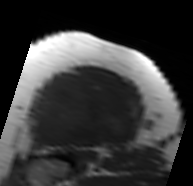
MRI of an extremity soft-tissue mass, one axial slice. Position 56 of 91 along the scan axis. MR volume resampled by the dataset authors to the PET/CT grid (not the native acquisition matrix). 3.27 mm slice thickness. 193 × 186 image matrix. Female patient. From the clinical record (not read from this slice): histological type: malignant solitary fibrous tumor; grade: intermediate; site of the primary tumour: right thigh.
Annotated regions visible in this slice (expert contour drawn on MRI and transferred to this co-registered scan by the dataset authors):
- gross tumour volume including surrounding oedema: bounding box <31,72,139,148> (left, top, right, bottom; pixels)
- gross tumour volume (mass): <31,74,135,148>